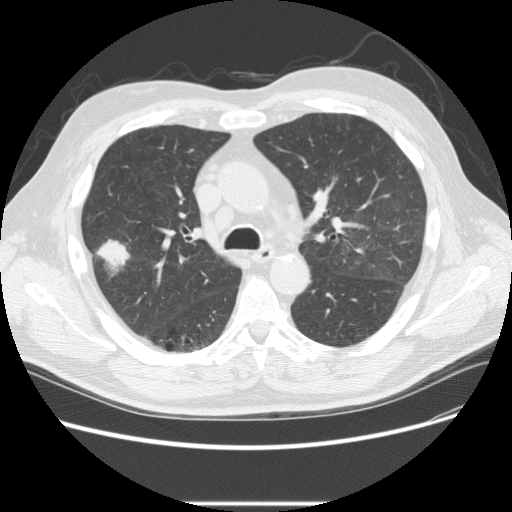
Low-dose screening chest CT, one axial slice. Position 152 of 233 along the scan axis. Lung window (W 1500 / L -600 HU). 512 × 512 image matrix.
Structures marked on this image (manually delineated by an expert):
- lesion 2 (tumor, upper lobe of right lung): box from (x=96, y=239) to (x=130, y=275) px